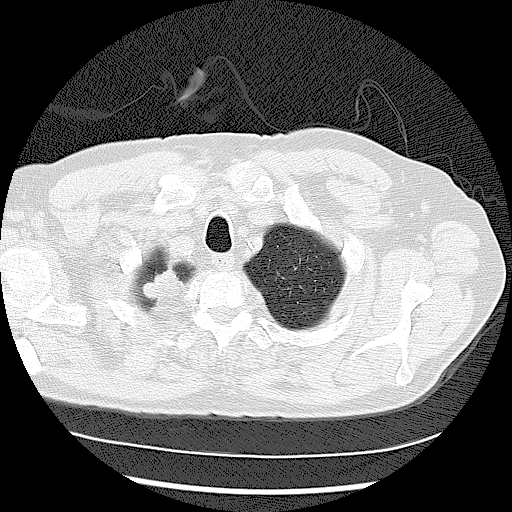
Low-dose screening chest CT, one axial slice. Position 106 of 122 along the scan axis. 120 kVp. Lung window (W 1500 / L -600 HU). 2.5 mm slice thickness. 512 × 512 image matrix, field of view 360 × 360 mm.
Outlined on this slice (outlined manually by an expert reader):
- lesion 2 (tumor, upper lobe of right lung): bounding box <141,270,182,311> (left, top, right, bottom; pixels)